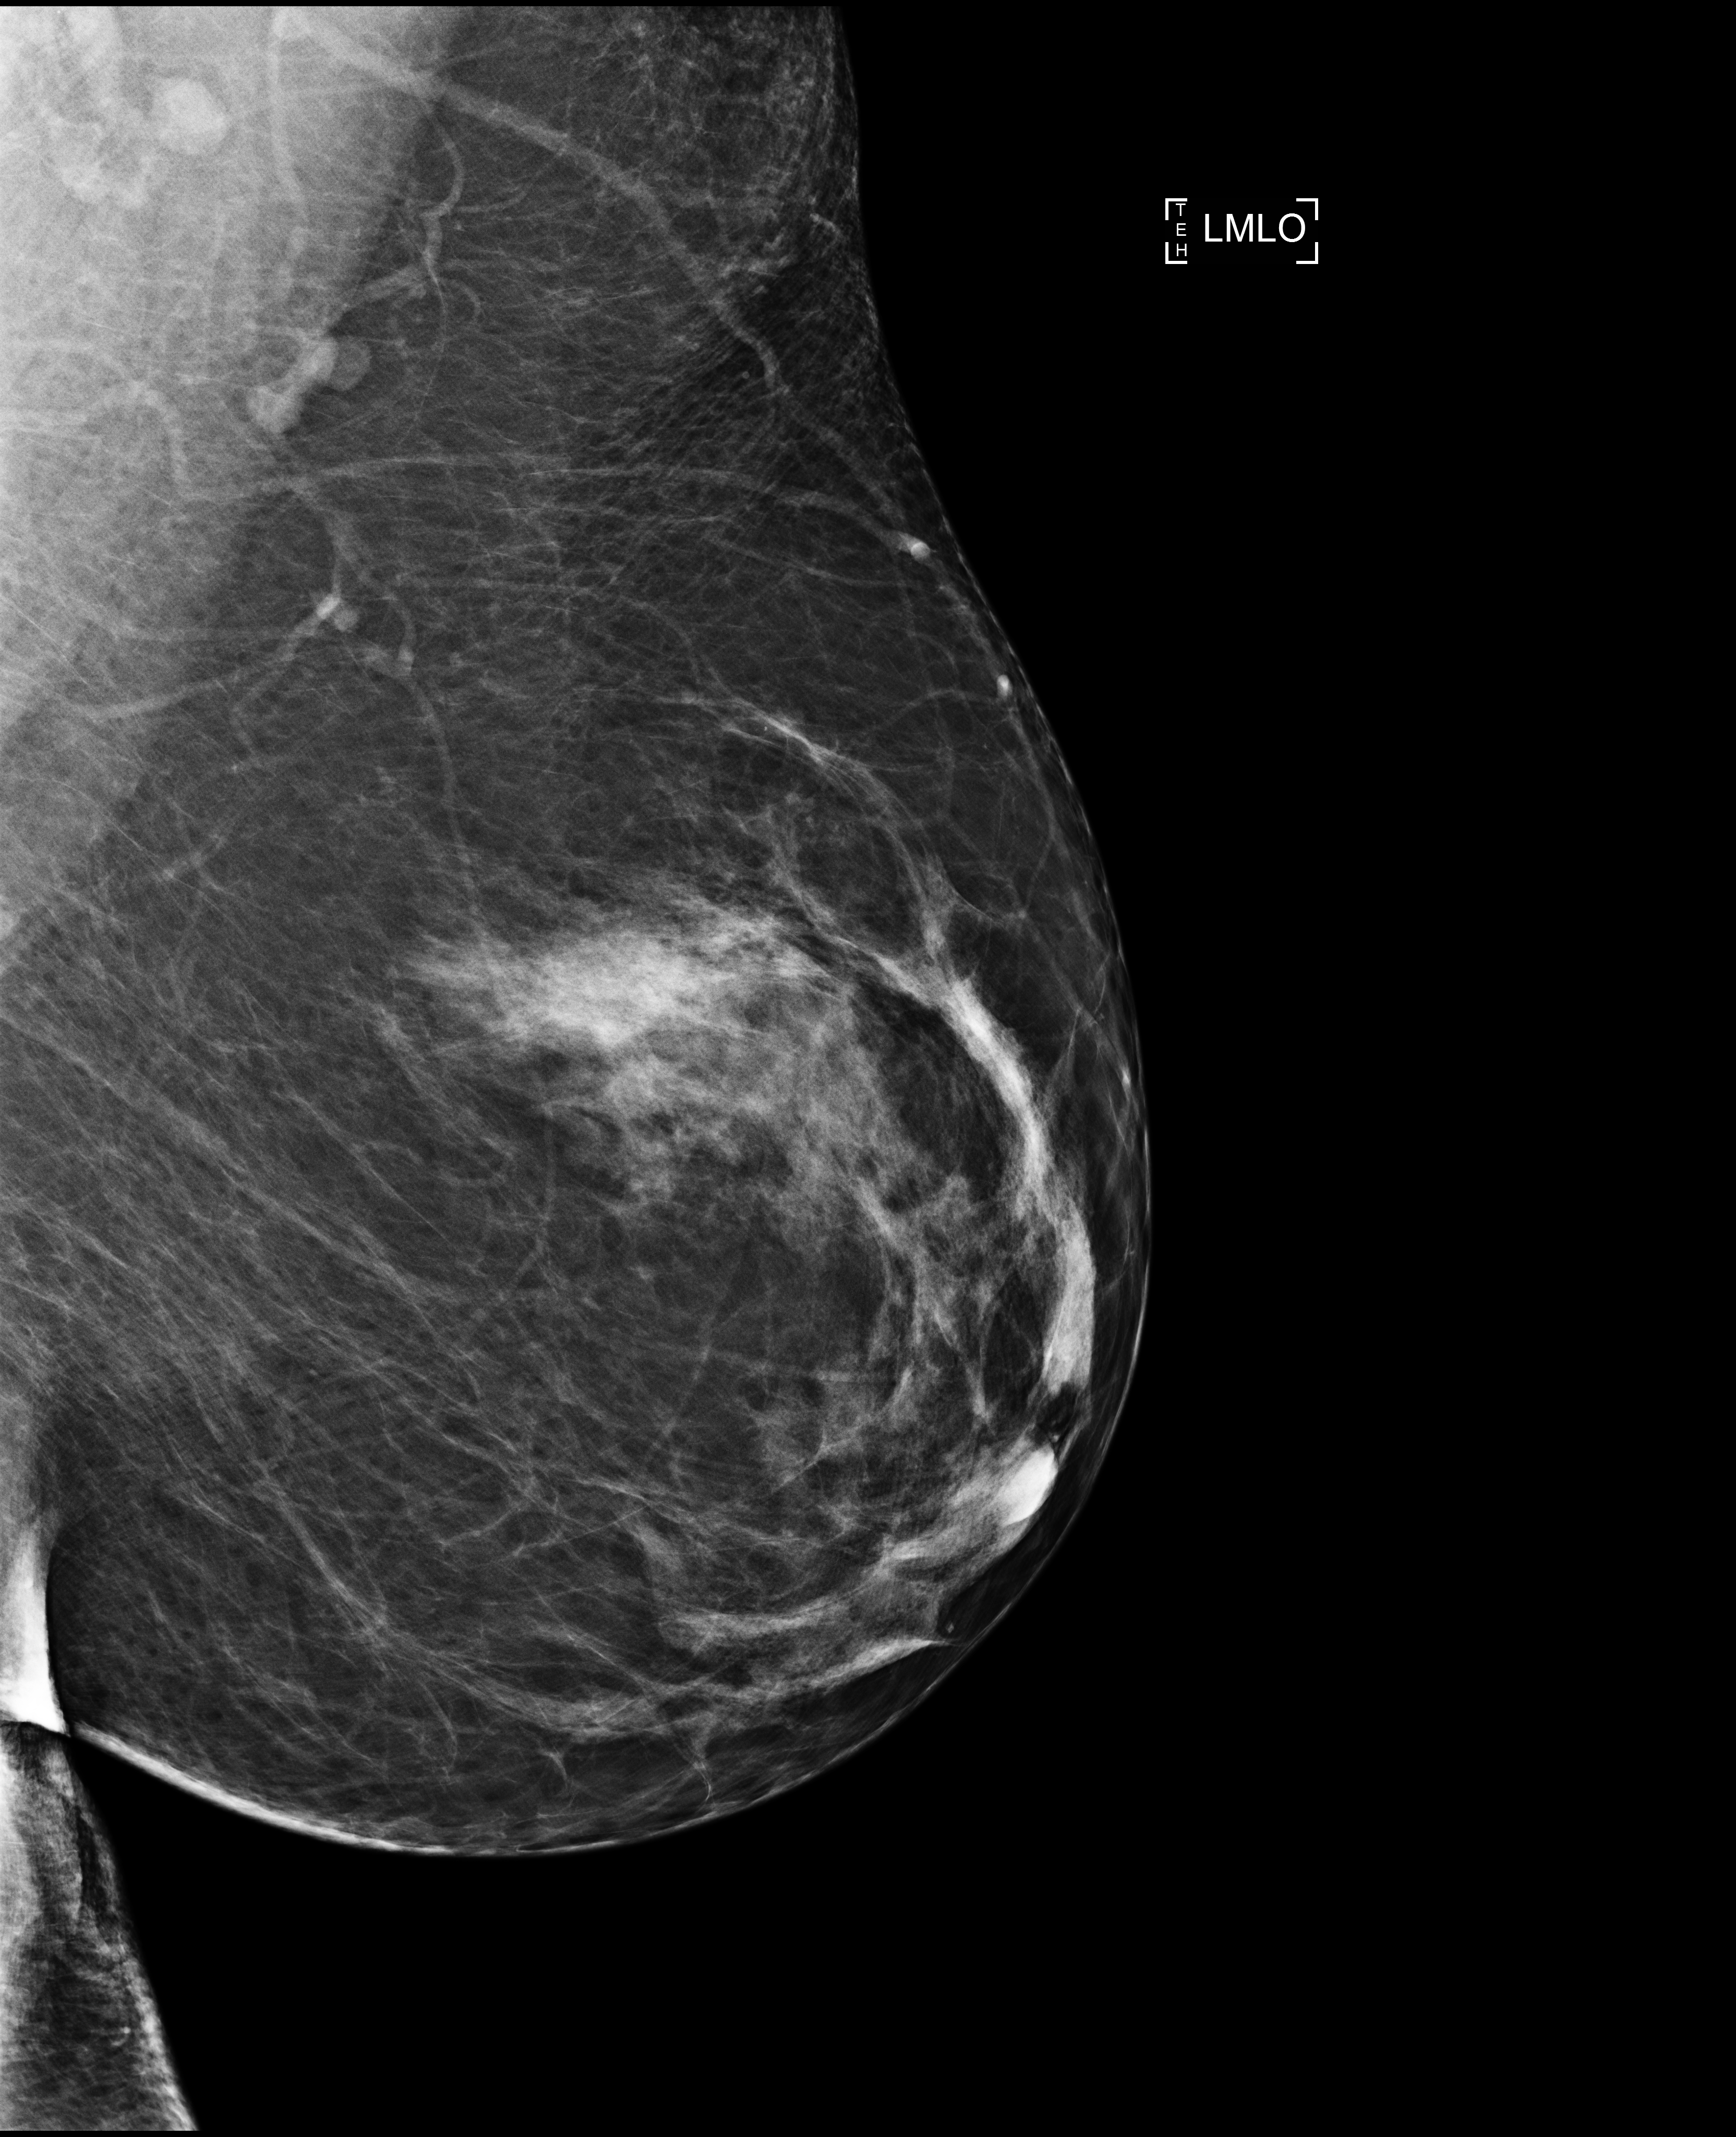
Screening examination; system: Selenia Dimensions. Patient aged 65 years (female).
Image type: full-field digital mammogram. Breast: left. Projection: MLO view.